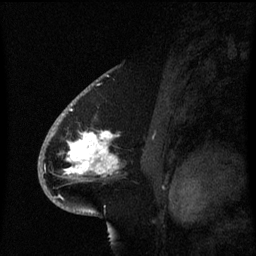
Breast MRI (dynamic contrast-enhanced), one sagittal slice; position 40 of 60 along the scan axis; dynamic contrast-enhanced series, image 2 of 3 at this slice position (ordered by acquisition); 1.5 T; TE 4.2 ms, TR 8.4 ms; 2.1 mm slice thickness; 256 × 256 image matrix. Patient: female, 53 years. From the clinical record (not read from this slice): setting: breast cancer imaged before/during neoadjuvant chemotherapy; receptor status: HR-positive, HER2-negative.
Annotated regions visible in this slice (semi-automatically segmented with operator editing):
- analysis volume of interest (the breast-tissue region the enhancement analysis was run in; not a lesion): box from (x=49, y=108) to (x=124, y=201) px
- tumour enhancement mask (voxels above the 70 % enhancement threshold inside the analysis volume of interest): (x=67, y=132)–(x=120, y=175)